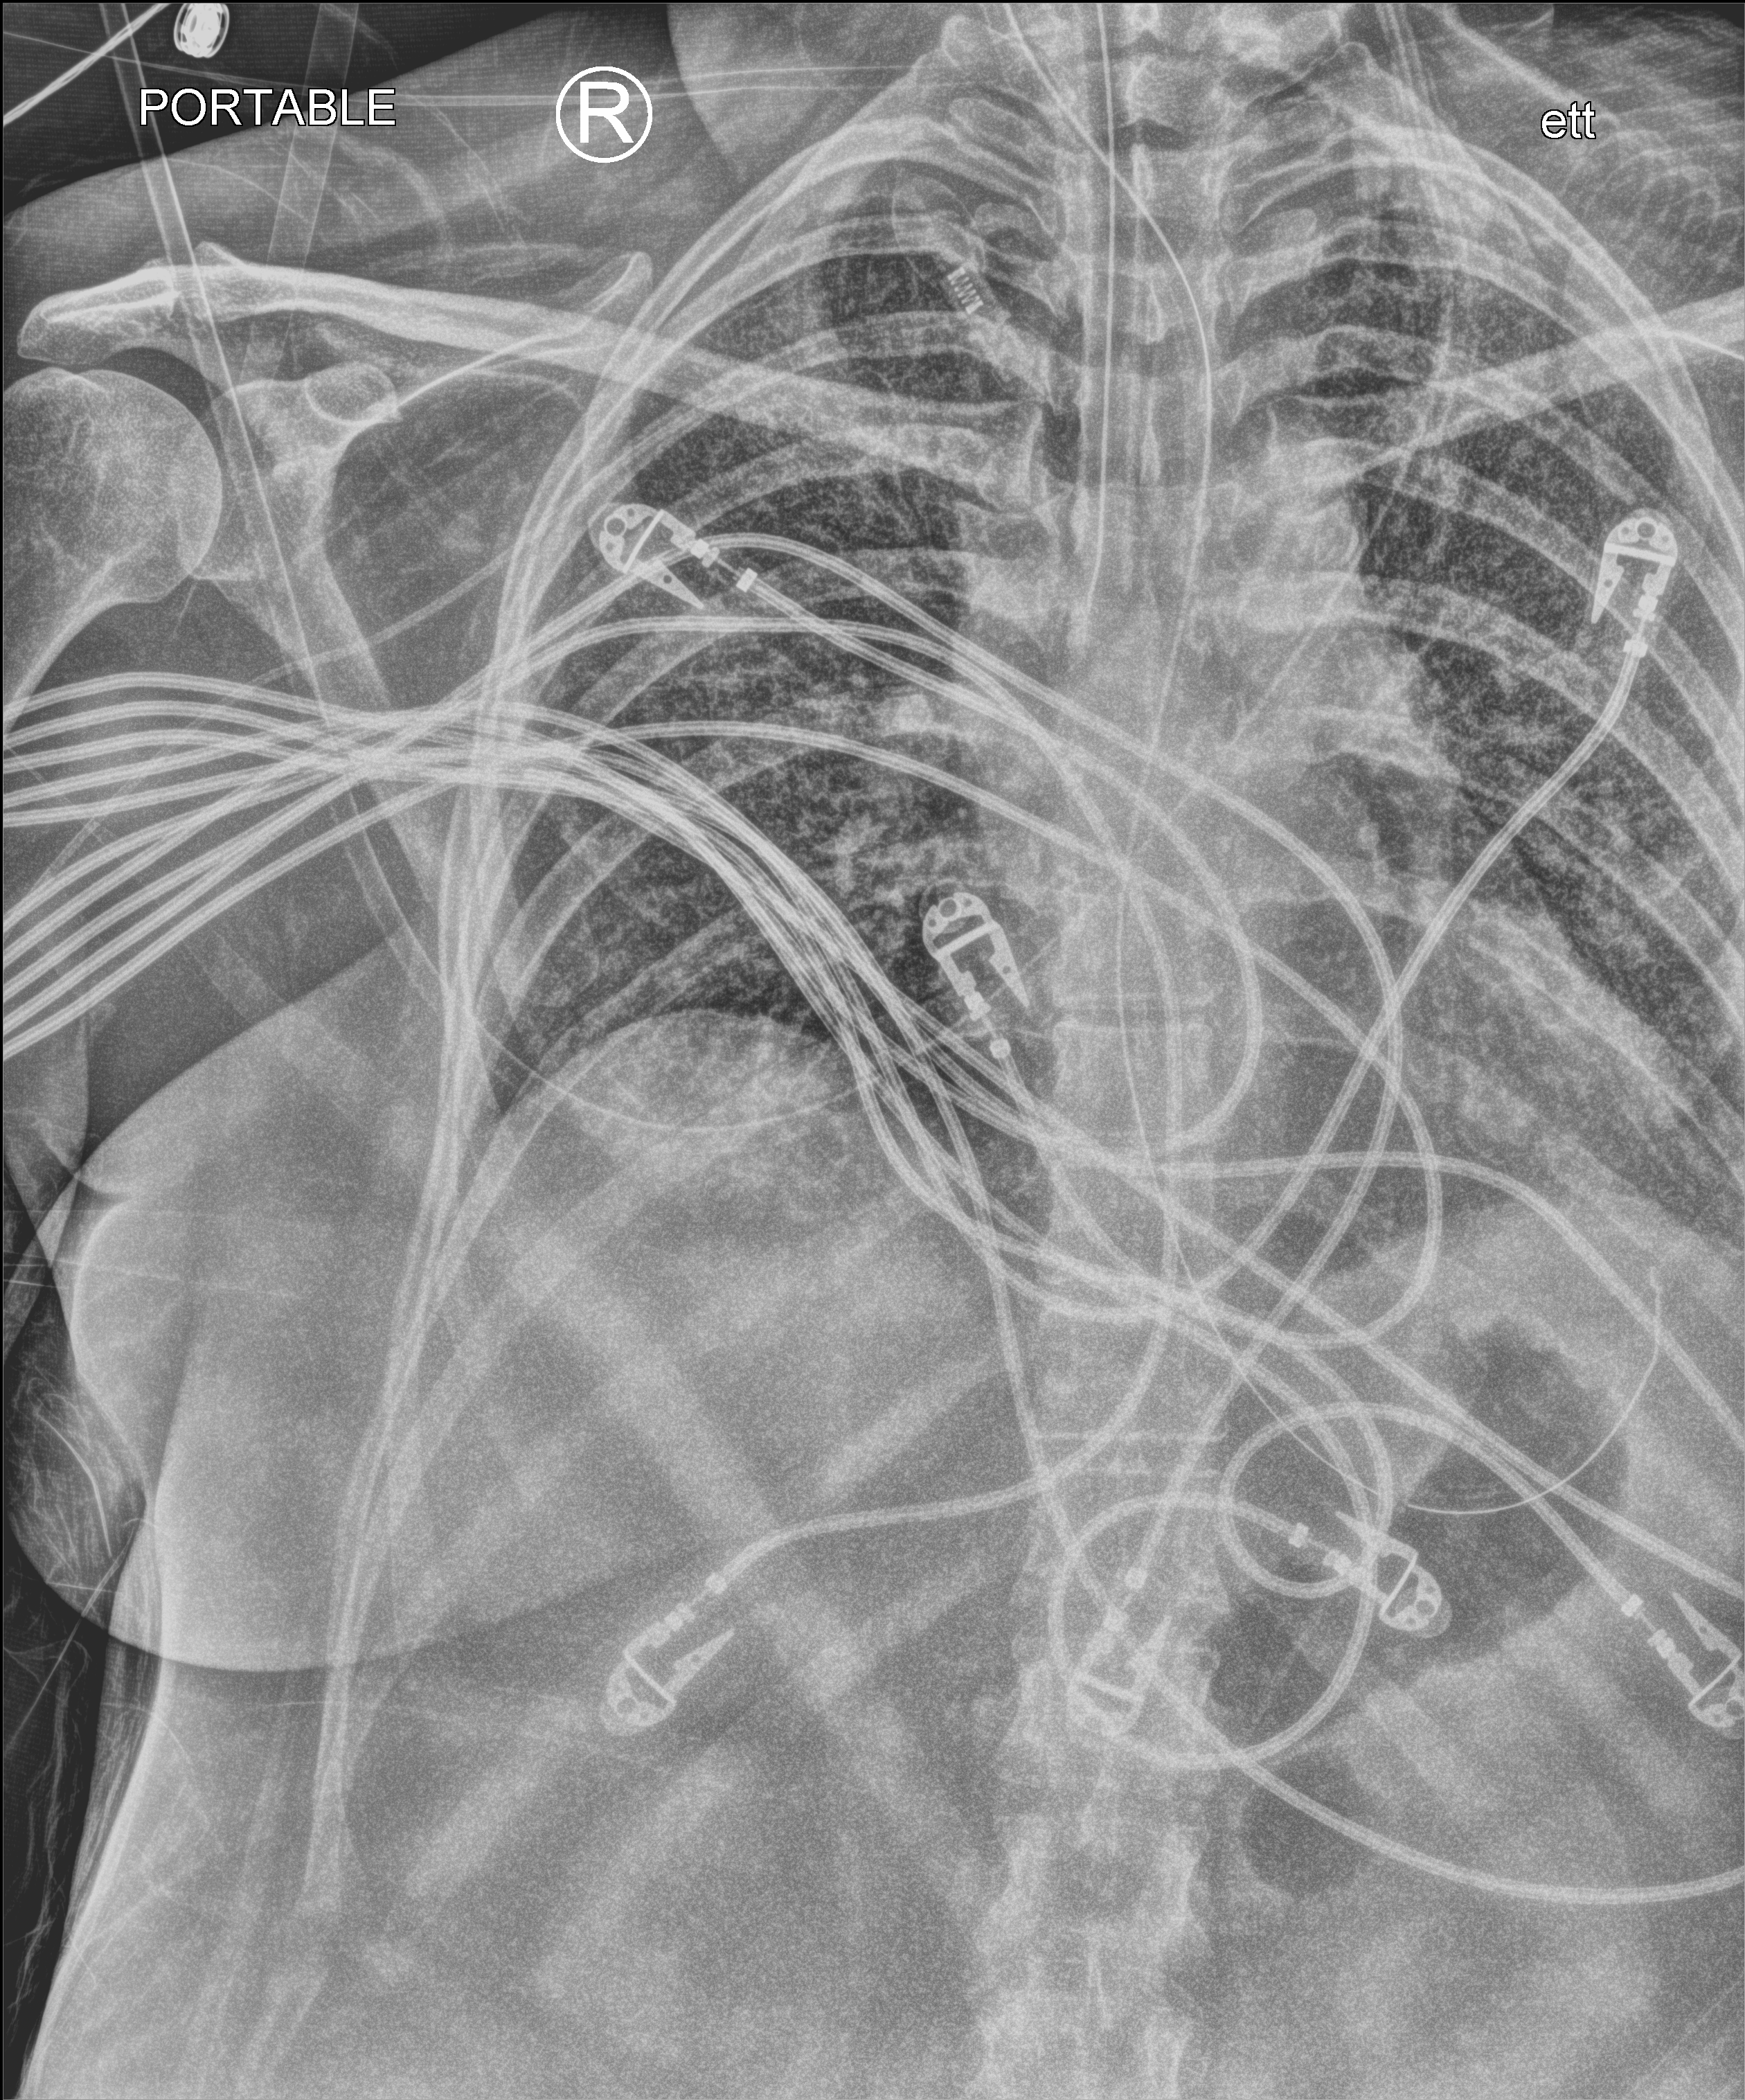
Chest X-ray (portable); anteroposterior (AP) projection. Female patient hospitalised with COVID-19, age 18–59 years.
Hospital-stay facts (about this admission, not read from this image; timing relative to this image not recorded):
- other chronic lung disease (admission record): yes